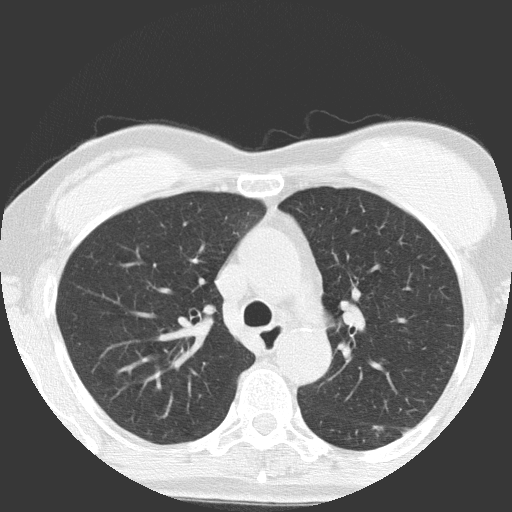
Chest CT (low-dose screening protocol), one axial image. First (baseline) screen. Lung window (W 1500 / L -600 HU). 2 mm slice thickness. 512 × 512 image matrix, field of view 300 × 300 mm. Female, age 64 years at enrolment. Former smoker at enrolment.
• Expert-annotated lung lesion, box from (x=327, y=402) to (x=417, y=472) px.
• Reader record for this screening exam (exam-level; its link to the box is not recorded): non-calcified nodule or mass ≥4 mm, right upper lobe, 4 × 4 mm, poorly defined margins, ground glass attenuation.
• Note: the box lies in the patient's left hemithorax on this image, whereas the reader's record names the right lung; they may be different findings.
• Official screen result: positive, change unspecified: nodule(s) >= 4 mm or enlarging nodule(s), mass(es), or other non-specific abnormalities suspicious for lung cancer.